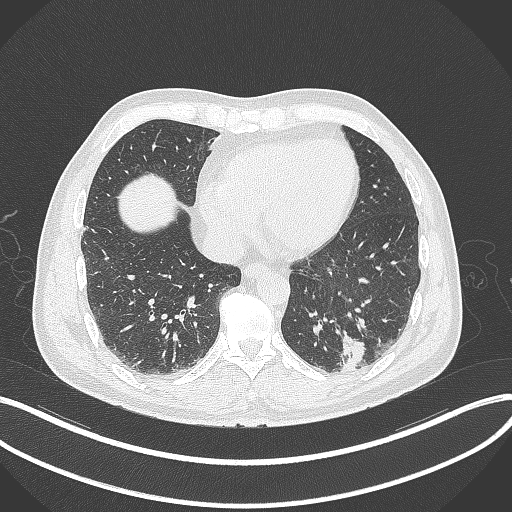
Chest CT, one axial slice; slice 87 of 300 in the series (ordered by position); reconstruction kernel B70f; lung window (W 1500 / L -600 HU); 512 × 512 image matrix, field of view 400 × 400 mm. Patient: male, 54 years. From the clinical record (not read from this slice): clinical TNM (as recorded): T1c N0 M1; histopathological grade: G3.
Annotated regions visible in this slice (bounding box drawn by a radiologist):
- lung tumour (recorded histology: adenocarcinoma): bounding box [x1, y1, x2, y2] px = [335, 330, 365, 375]